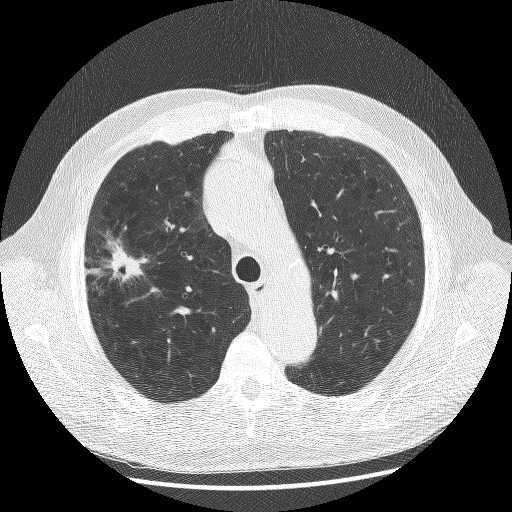
Axial slice from a low-dose chest CT screening exam, baseline annual screen, lung window (W 1500 / L -600 HU), 2.5 mm slice thickness, 120 kVp, slice 41 of 175 in the series, 512 × 512 image matrix. Male, age 70 years at enrolment. Current smoker at enrolment.
- Expert-annotated lung lesion, bounding box [x1, y1, x2, y2] px = [77, 234, 147, 306].
- The screening reader recorded 2 non-calcified nodules or masses ≥4 mm on this exam (left upper lobe, right upper lobe); which of them this box marks is not recorded.
- Participant outcome: lung cancer diagnosed 23 days after this screen — non-small cell carcinoma, right upper lobe, poorly differentiated (G3), stage IA (AJCC 6th edition), 20 mm at pathology.